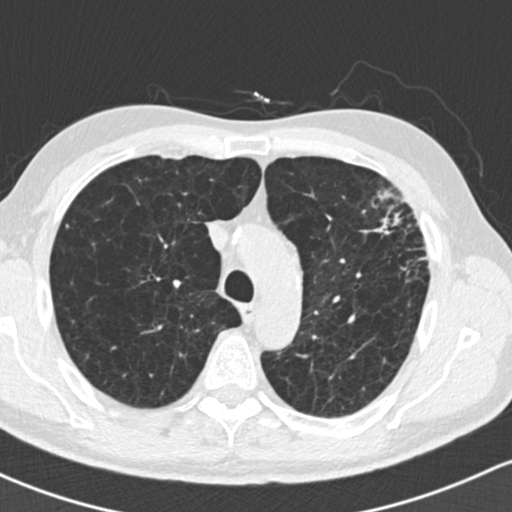
Axial slice from a low-dose chest CT screening exam, baseline annual screen, lung window (W 1500 / L -600 HU), 2 mm slice thickness, slice 48 of 162 in the series. Male, age 61 years at enrolment. Former smoker at enrolment.
Expert-annotated lung lesion, bounding box (x1, y1, x2, y2) in pixels: (352, 183, 442, 287). The exam's reader record, not a measurement of the box and not confirmed to be the same lesion: non-calcified nodule or mass ≥4 mm, left upper lobe, 35 × 35 mm, spiculated (stellate) margins, soft tissue attenuation. Official screen result: positive, change unspecified: nodule(s) >= 4 mm or enlarging nodule(s), mass(es), or other non-specific abnormalities suspicious for lung cancer.